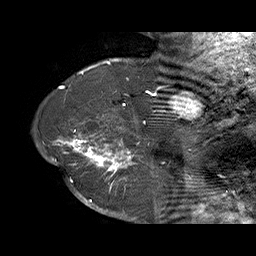
Breast MRI (dynamic contrast-enhanced), one sagittal slice; position 54 of 70 along the scan axis; dynamic contrast-enhanced series, time point 2 of 6 at this slice position (early post-contrast); 1.5 T; TE 4.5 ms, TR 32.4 ms; 3 mm slice thickness; 256 × 256 image matrix. Female patient. Case-level facts recorded for this patient, not image findings: setting: breast cancer imaged before/during neoadjuvant chemotherapy; receptor status: HR-positive, HER2-negative.
Structures marked on this image (semi-automatically segmented with operator editing):
- analysis volume of interest (the breast-tissue region the enhancement analysis was run in; not a lesion): bounding box (x1, y1, x2, y2) in pixels: (71, 128, 159, 202)
- tumour enhancement mask (voxels above the 100 % enhancement threshold inside the analysis volume of interest): (71, 130, 150, 202)